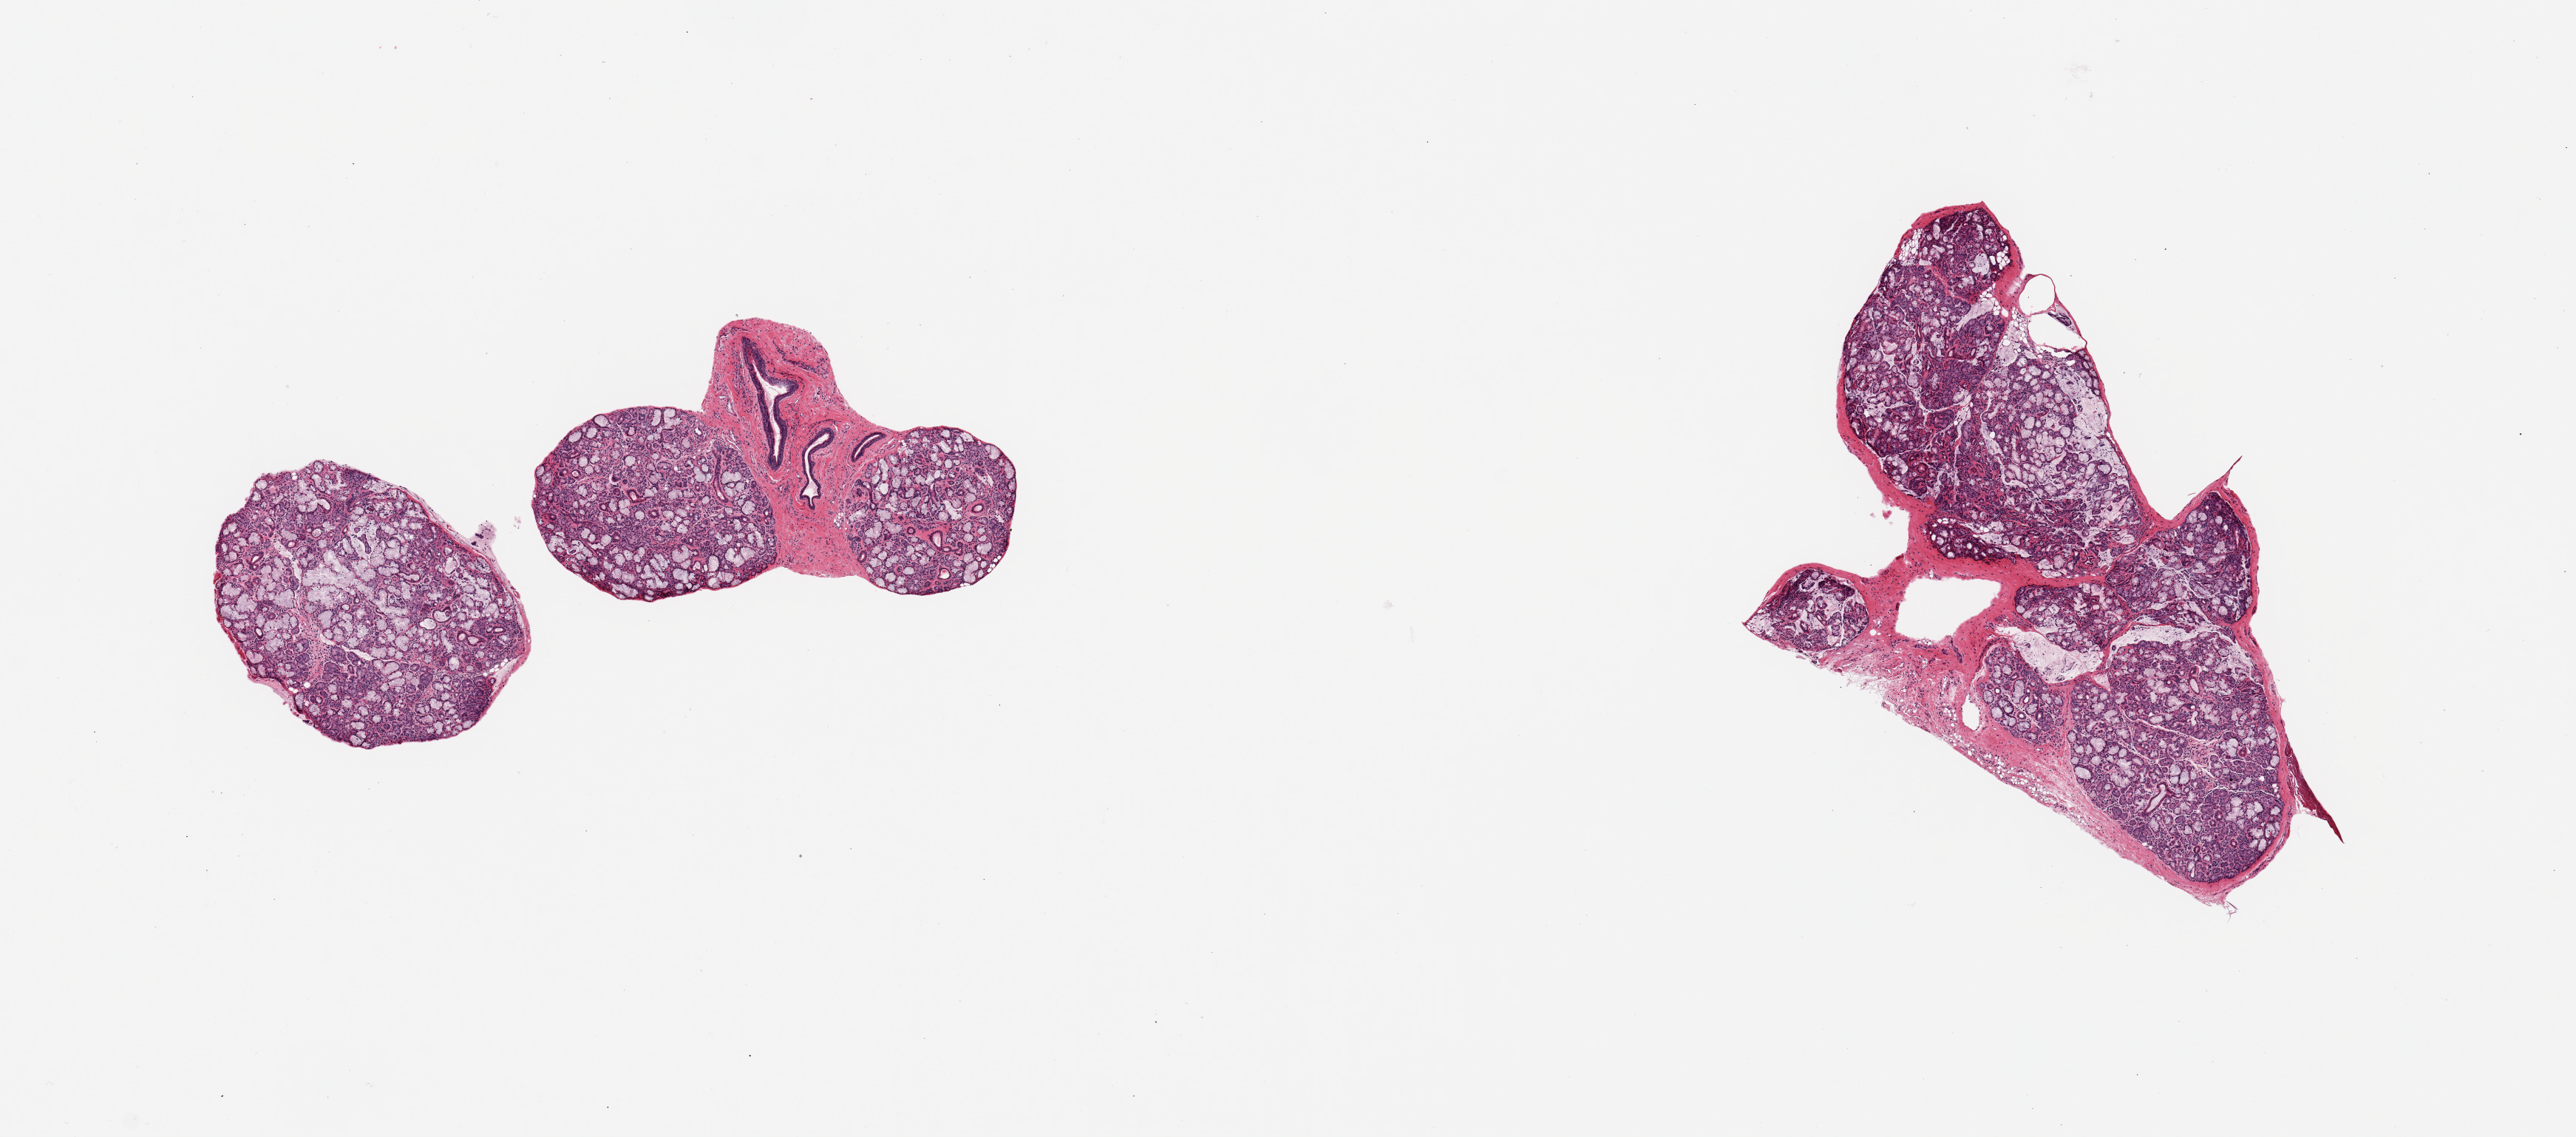
Haematoxylin and eosin whole-slide image, brightfield — whole scanned area (about 13.8 x 6.1 mm) shown as a low-resolution overview; PAXgene-fixed paraffin-embedded (PFPE) section; target tissue: minor salivary gland; tissue donor sample.
Reviewer comment on this tissue sample: 2 pieces, ~85-90% glandular elements, good specimens.